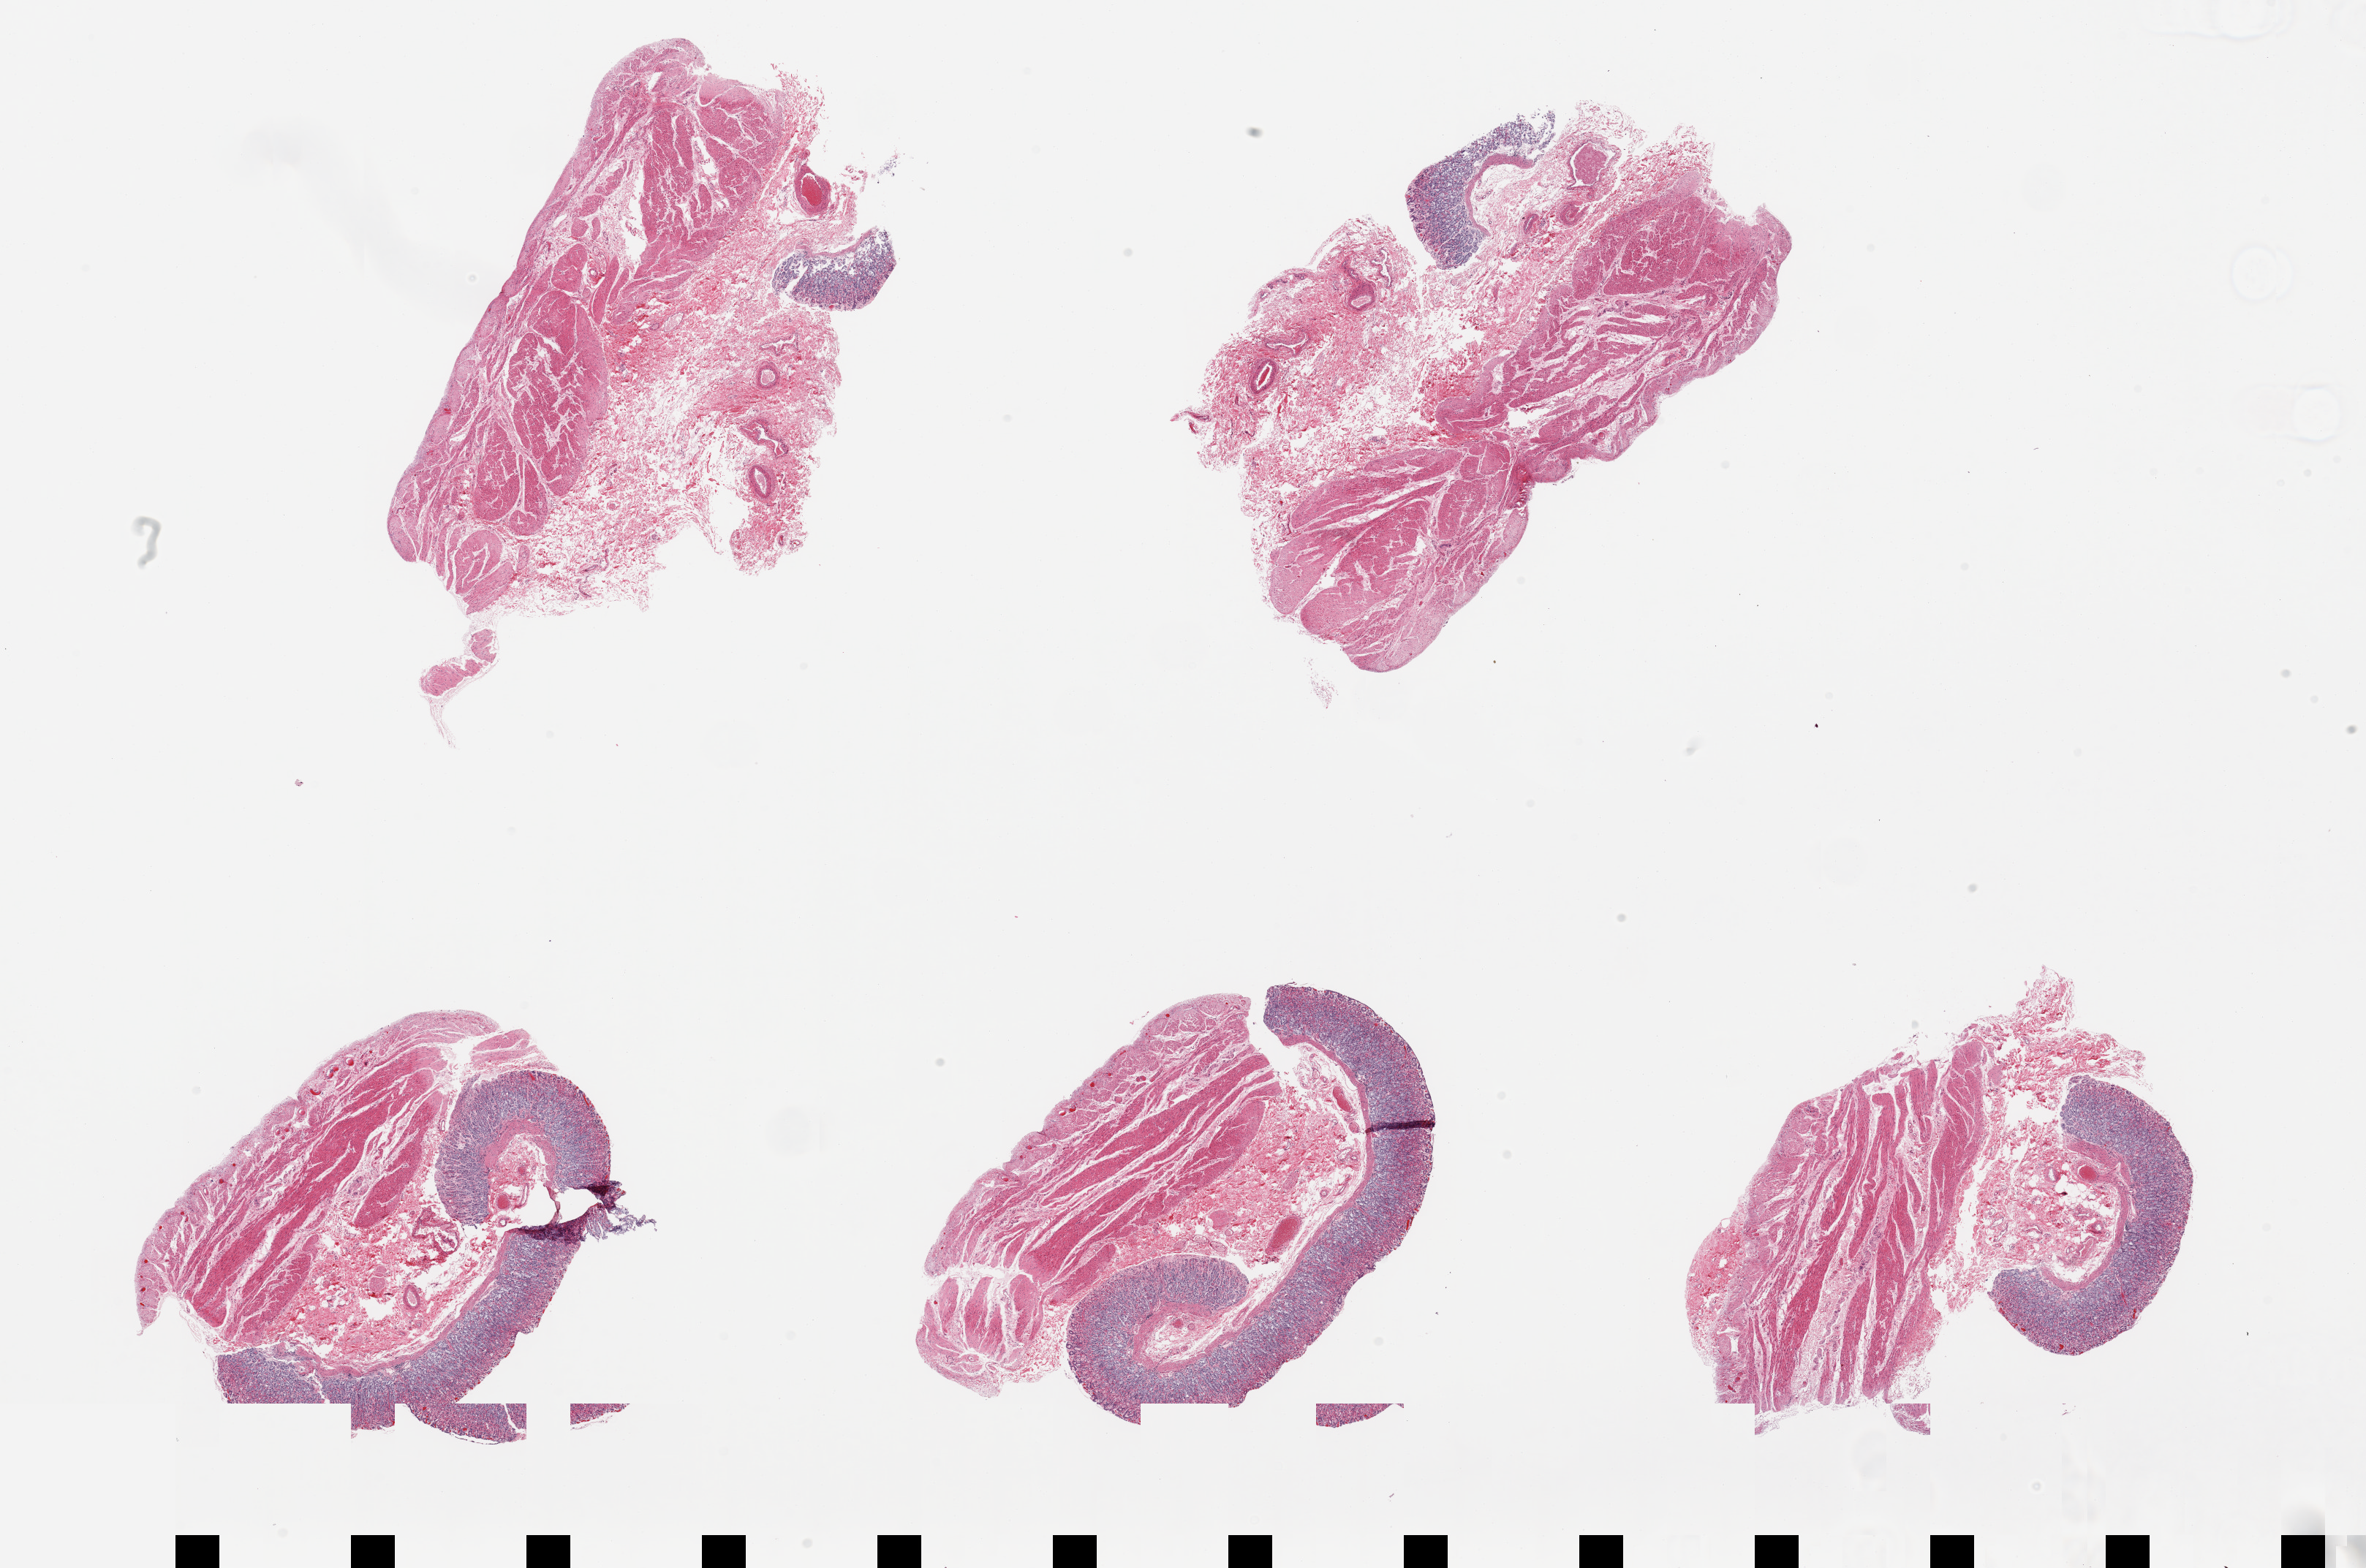
Digitized hematoxylin and eosin (H&E)-stained section, brightfield, a low-resolution overview of the entire scanned area, about 25.6 x 17.0 mm, PAXgene-fixed, paraffin-embedded tissue, section of stomach (target tissue), donor tissue sample. Male donor.
Review note (as recorded): 5 pieces; full thickness sections, but 2 include only small portion of mucosa.